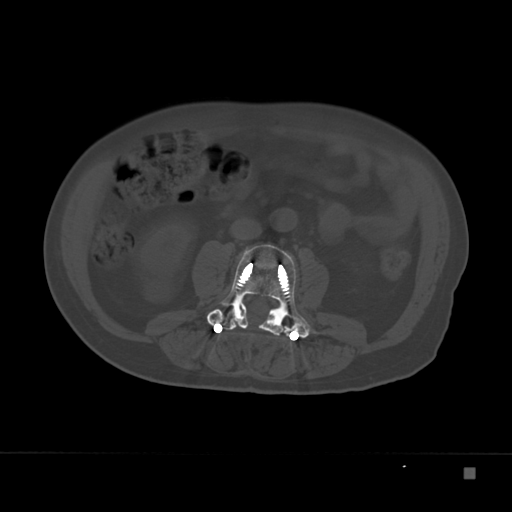
CT including the spine, one axial slice. Position 67 of 332 along the scan axis. Reconstruction kernel Br40s. Bone window (W 1800 / L 400 HU). 1.5 mm slice thickness. 512 × 512 image matrix, field of view 389 × 389 mm. Patient: male, 72 years. Case-level facts recorded for this patient, not image findings: primary cancer: skeletal.
Annotated regions visible in this slice (semi-automatically segmented with operator editing):
- L3 vertebra: bounding box <207,244,317,340> (left, top, right, bottom; pixels)